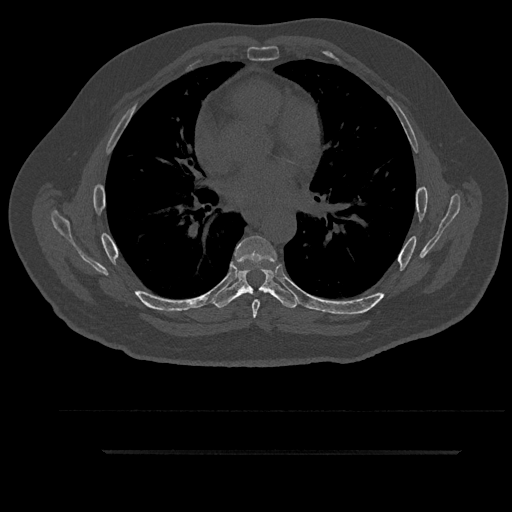
CT including the spine, one axial slice; slice 551 of 797 in the series (ordered by position); reconstruction kernel Br40s/3; 120 kVp; bone window (W 1800 / L 400 HU); 0.5 mm slice thickness; 512 × 512 image matrix, field of view 432 × 432 mm. Patient: male, 63 years. From the clinical record (not read from this slice): primary cancer: renal.
Structures marked on this image (semi-automatic segmentation, software-assisted and operator-edited):
- T5 vertebra: bounding box (x1, y1, x2, y2) in pixels: (261, 287, 266, 291)
- T6 vertebra: (235, 236, 277, 318)
- T7 vertebra: (213, 266, 299, 308)